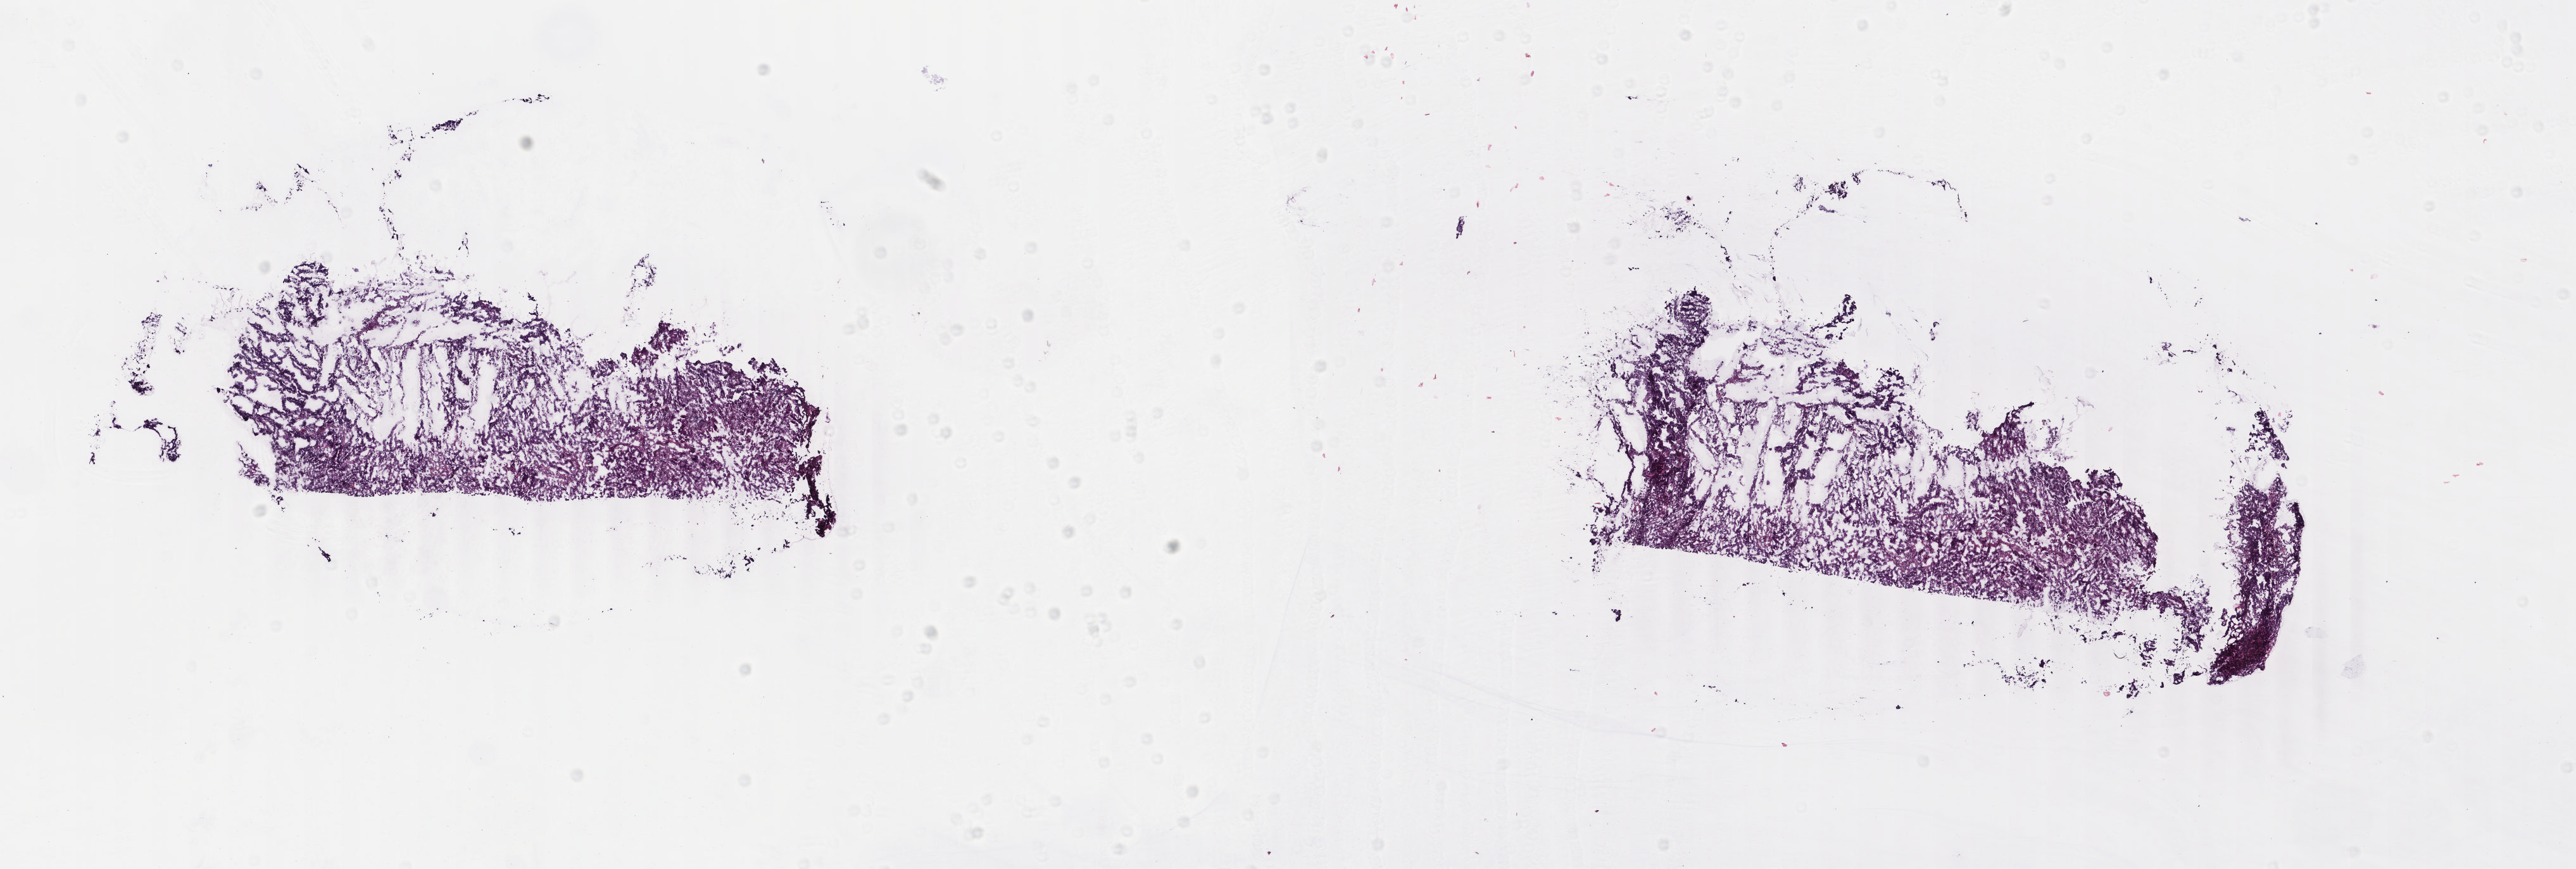
Hematoxylin and eosin (H&E) stained whole-slide image, shown as a low-resolution overview of the whole scanned area (about 16.2 x 5.5 mm, slide scanned at 40x). Frozen section from the top of the tissue portion. Primary tumour sample from the uterus. Female, age 37 years at initial diagnosis. Histologic grade: G2 (moderately differentiated). Slide review estimates, as recorded: tumour cells 80%, tumour nuclei 80%, normal cells 0%, stromal cells 10%, necrosis 10%. Infiltration values recorded for this section: lymphocyte infiltration 10%, monocyte infiltration 0%, neutrophil infiltration 0%.
Lymph nodes positive (case pathology): 0 of 13 examined. Pathologic diagnosis: Endometrioid adenocarcinoma, NOS (endometrium). FIGO stage: IIIA.